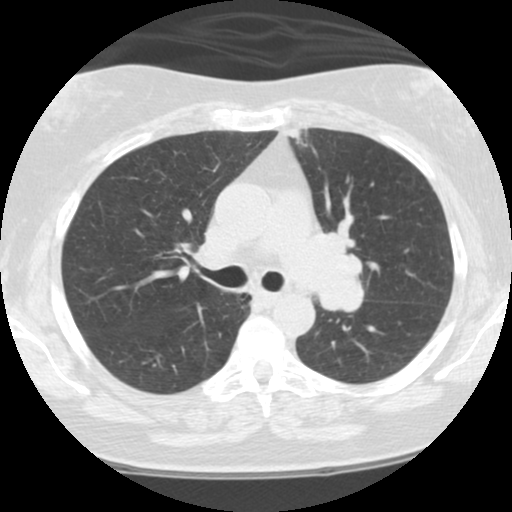
Chest CT (low-dose screening protocol), one axial image; third screening round (two years after baseline); lung window (W 1500 / L -600 HU); standard (soft-tissue) reconstruction kernel (STANDARD); slice 39 of 108 in the series; 512 × 512 image matrix, field of view 300 × 300 mm. Female participant, aged 59 years at enrolment.
Expert-annotated lung lesion, box from (x=285, y=213) to (x=382, y=325) px. Screening reader's record for this exam: no non-calcified nodule ≥4 mm recorded. Later outcome: lung cancer diagnosed 192 days after this screen — small cell carcinoma, NOS, left upper lobe, left hilum, mediastinum, left main stem bronchus, stage IV (AJCC 6th edition), 63 mm at pathology.